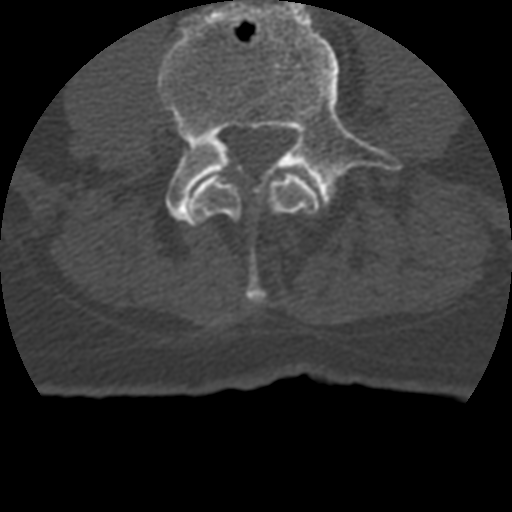
CT including the spine, one axial slice; slice 73 of 399 in the series (ordered by position); reconstruction kernel STANDARD; bone window (W 1800 / L 400 HU); 1.25 mm slice thickness; 512 × 512 image matrix, field of view 160 × 160 mm. Patient age 69 years. From the clinical record (not read from this slice): primary cancer: prostate.
Structures marked on this image (semi-automatically segmented with operator editing):
- L3 vertebra: bounding box [x1, y1, x2, y2] px = [190, 174, 320, 304]
- L4 vertebra: [158, 0, 406, 223]